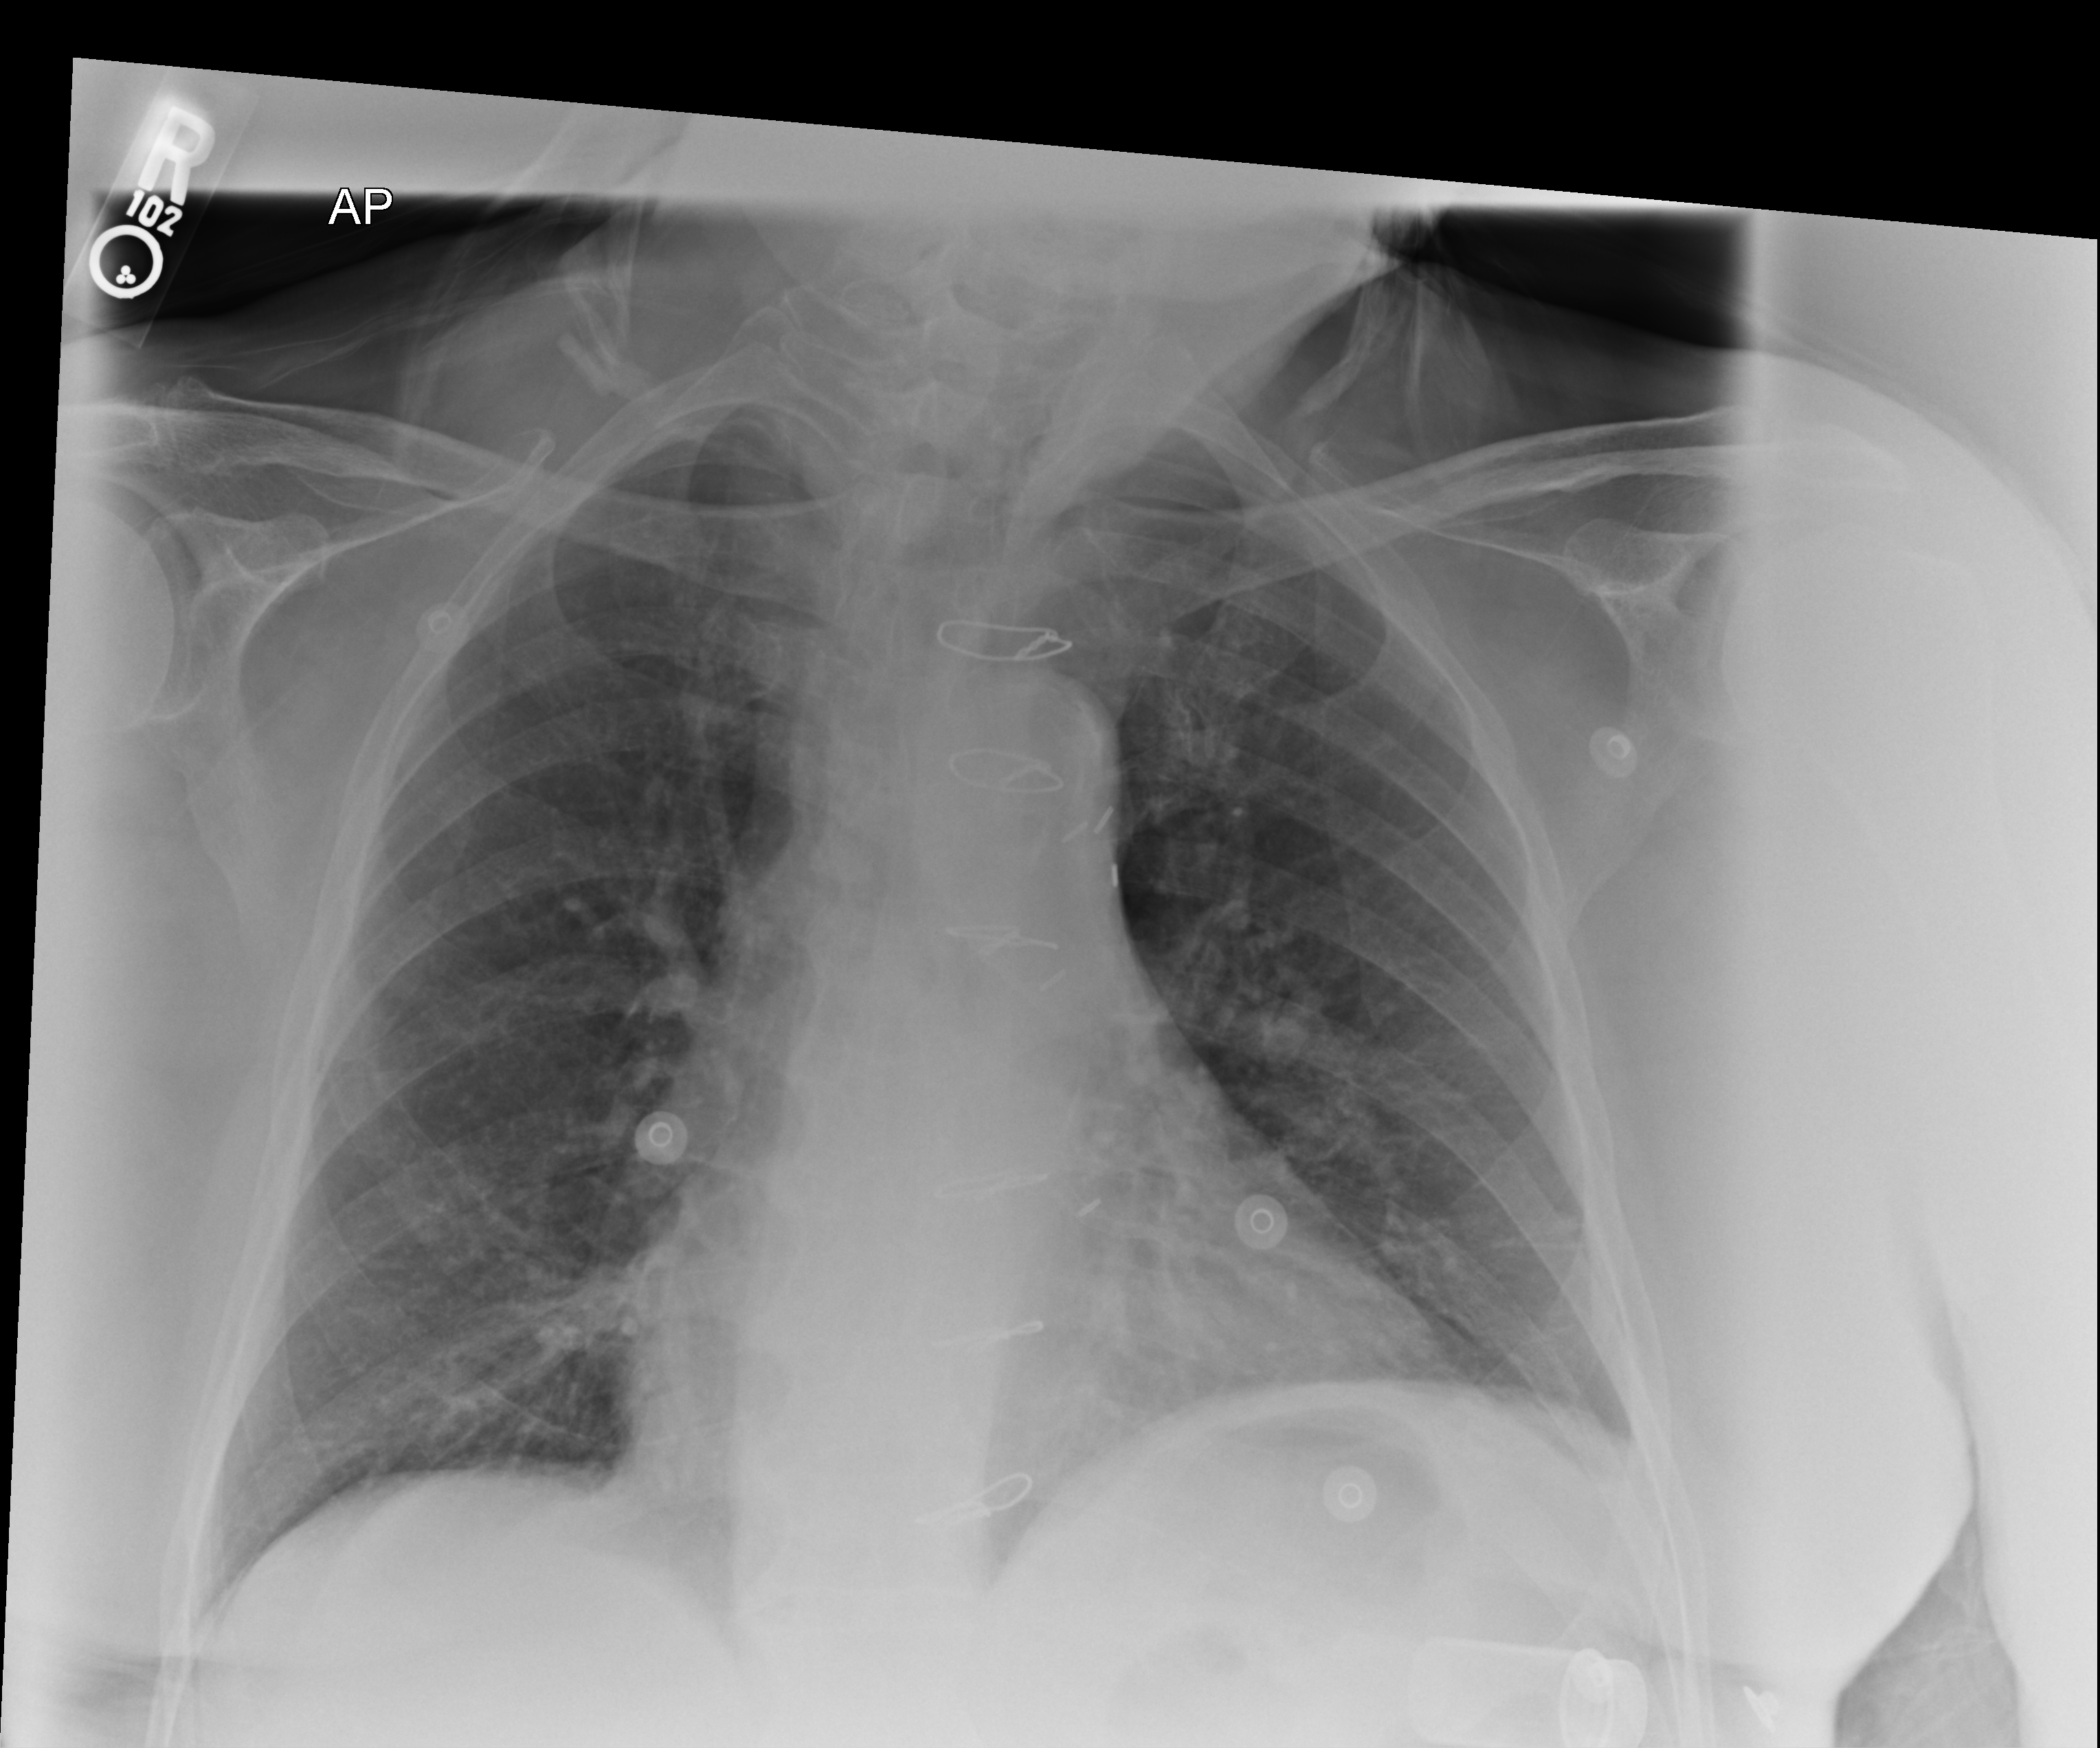
Chest radiograph; anteroposterior (AP) projection. Patient hospitalised with COVID-19; male, aged 75–90 years.
From the hospital-stay record, not from the radiograph (when in the stay this image was taken is not recorded):
- mechanically ventilated during this hospital stay: yes